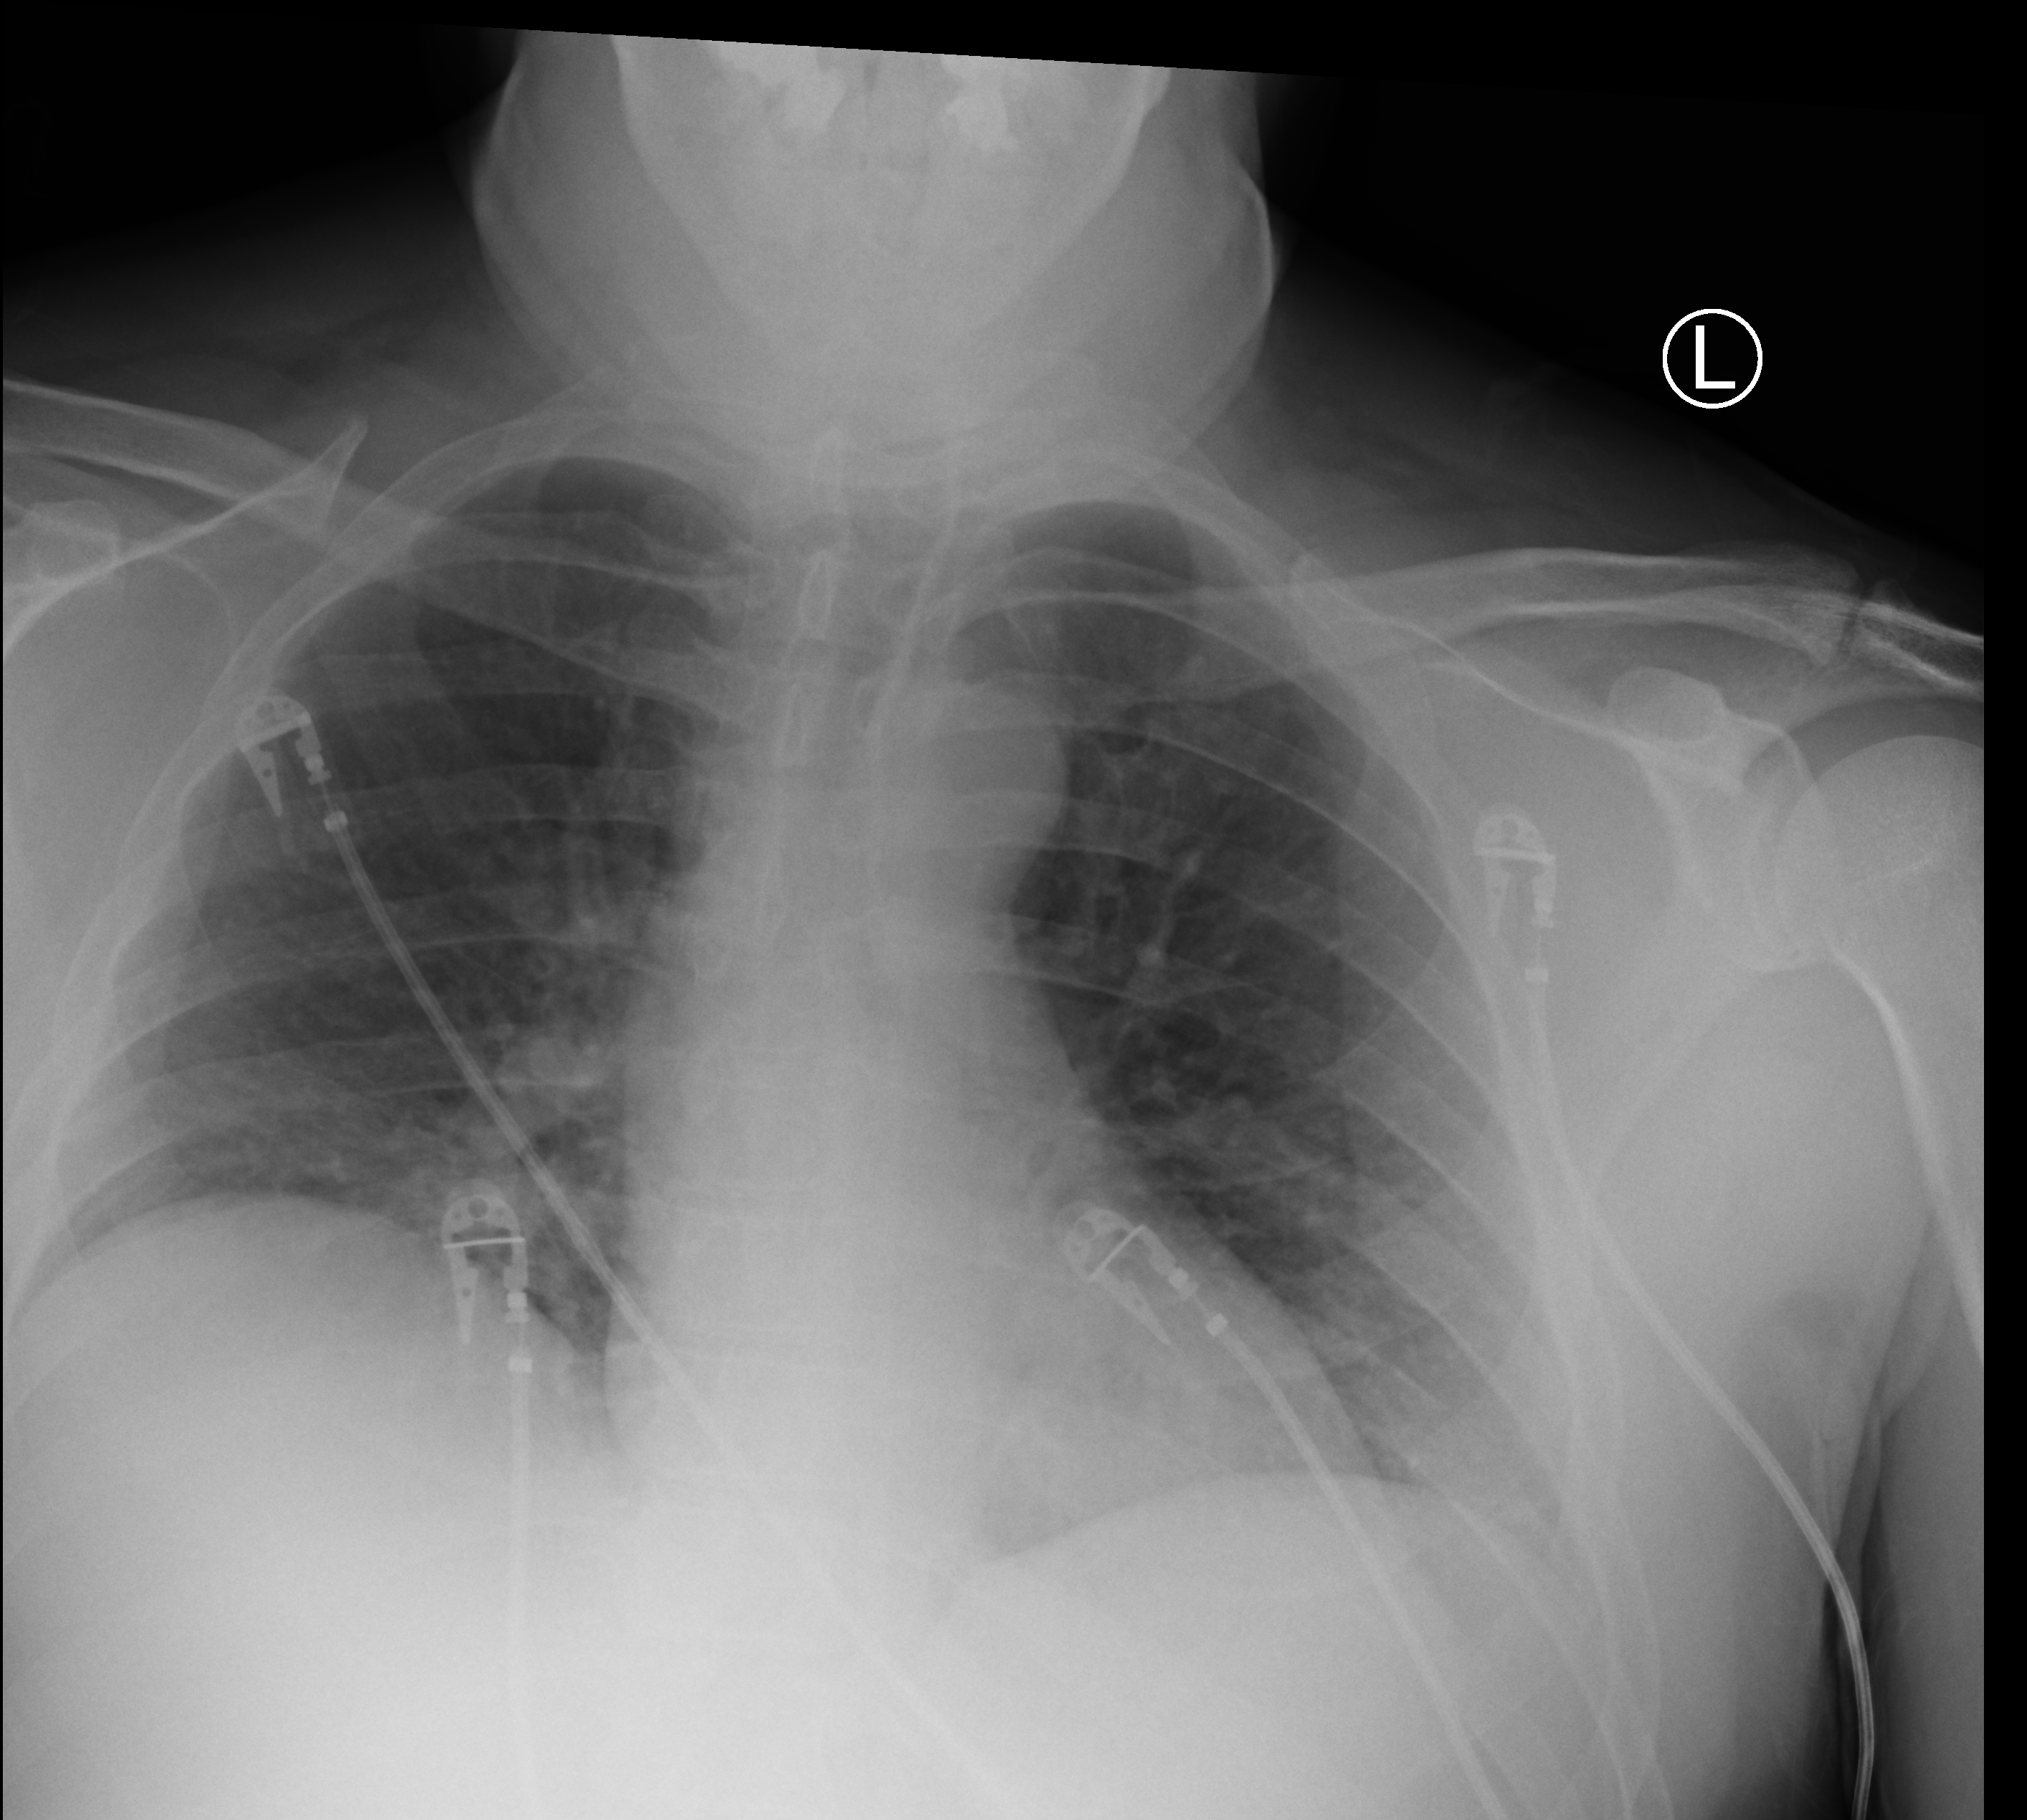
Bedside chest radiograph (computed radiography); anteroposterior (AP) projection. Male patient hospitalised with COVID-19, age 18–59 years.
From the hospital-stay record, not from the radiograph (when in the stay this image was taken is not recorded): length of hospital stay: 1 day.